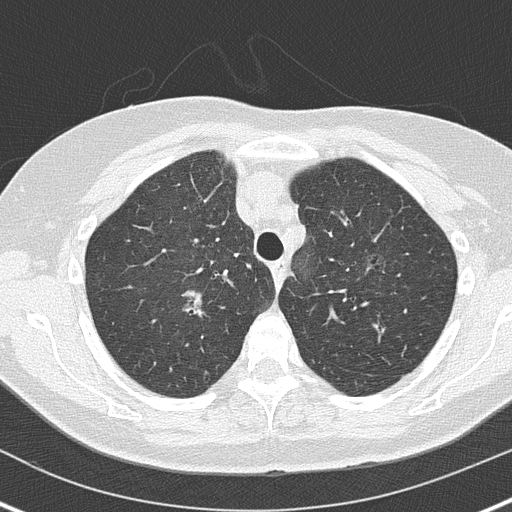
Chest CT (low-dose screening protocol), one axial image, baseline annual screen, lung window (W 1500 / L -600 HU), 2 mm slice thickness, slice 40 of 162 in the series. Female participant, aged 61 years at enrolment. Current smoker at enrolment.
• Expert reader's lesion annotation, bounding box (x1, y1, x2, y2) in pixels: (177, 287, 220, 326).
• Screening reader's record for this exam (one nodule recorded; not confirmed to be the boxed lesion): non-calcified nodule or mass ≥4 mm, right upper lobe, 8 × 5 mm, smooth margins, soft tissue attenuation.